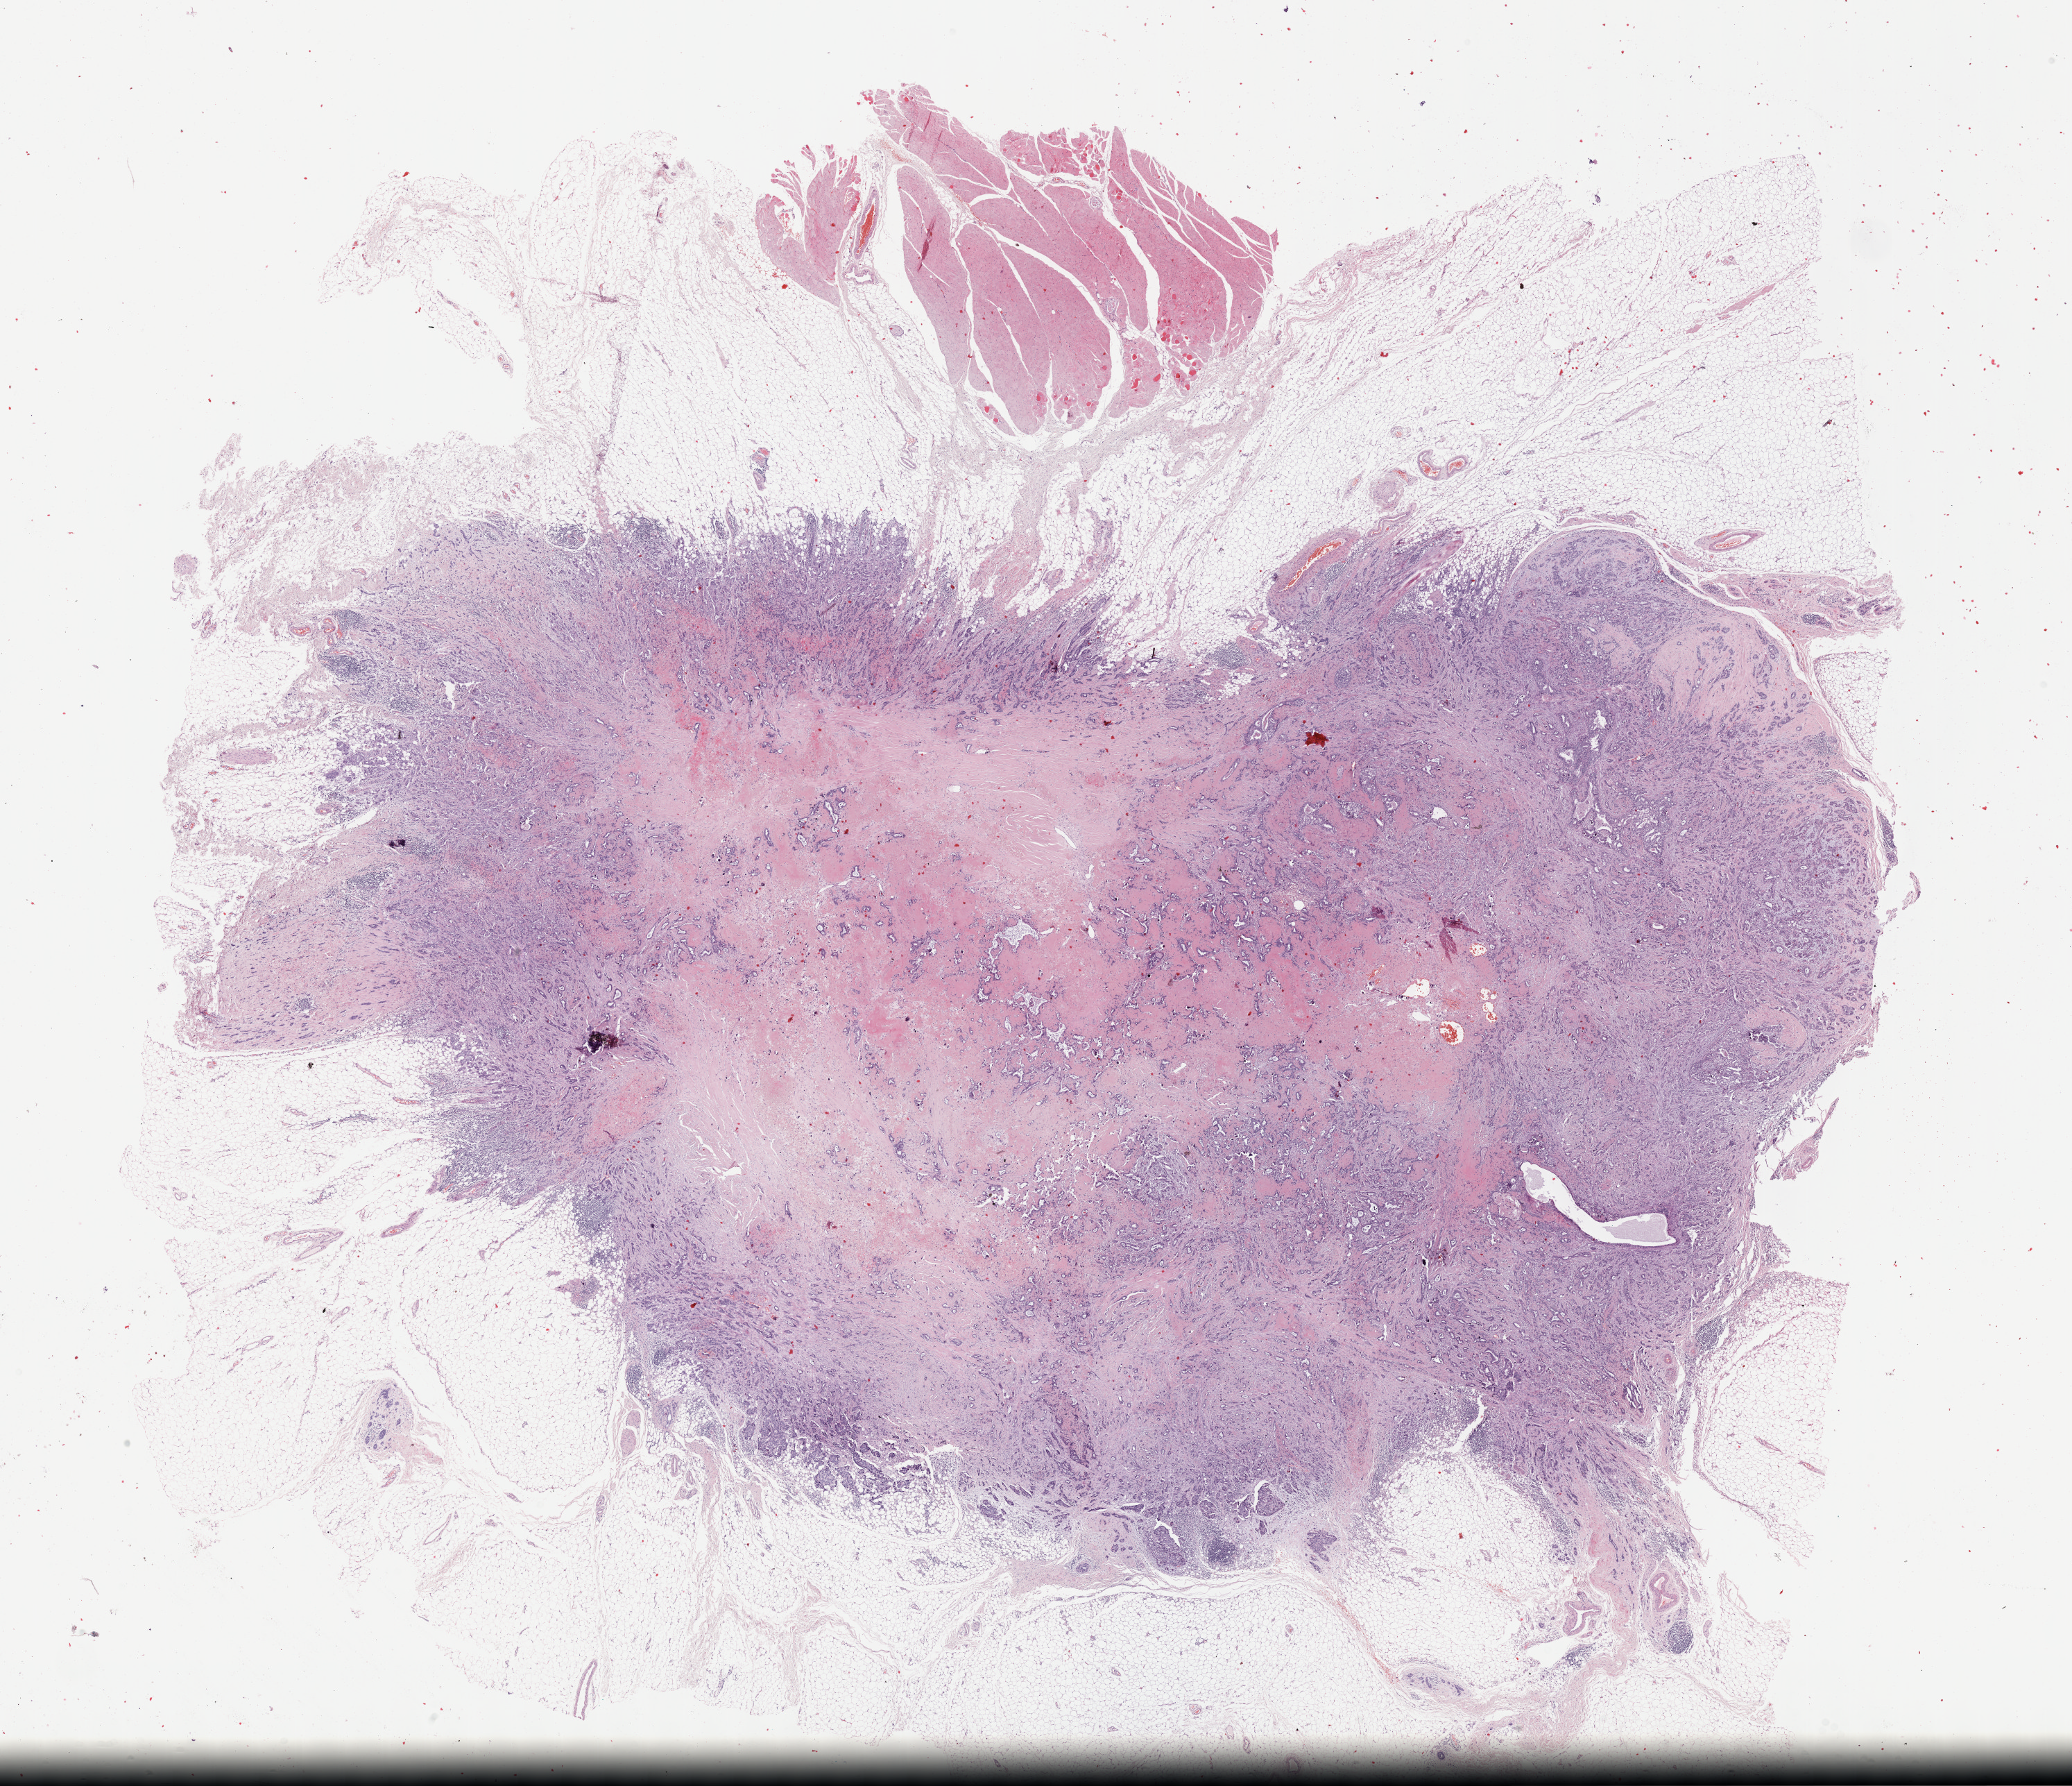
Hematoxylin and eosin (H&E) stained whole-slide image, low-resolution overview of the scanned area, about 24.2 x 20.8 mm (acquisition: 40x scan); formalin-fixed paraffin-embedded (FFPE) diagnostic section; breast, primary tumour sample. Female, age 62 years at initial diagnosis.
Lymph nodes positive (case pathology): 1 of 10 examined. Pathologic diagnosis: Infiltrating duct carcinoma, NOS. AJCC pathologic stage: IIB.